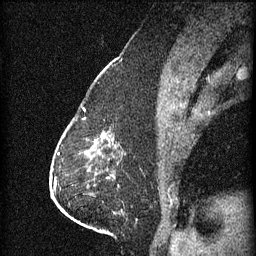
Breast MRI (dynamic contrast-enhanced), one sagittal slice; 3 images stored at this slice position (order not interpretable as contrast timing); 1.5 T; TE 4.2 ms, TR 11 ms; 1.5 mm slice thickness; 256 × 256 image matrix, field of view 180 × 180 mm. Female patient, age 63 years.
Structures marked on this image (semi-automatic segmentation, software-assisted and operator-edited):
- analysis volume of interest (the breast-tissue region the enhancement analysis was run in; not a lesion): bounding box (x1, y1, x2, y2) in pixels: (86, 130, 125, 153)
- tumour enhancement mask (voxels above the 70 % enhancement threshold inside the analysis volume of interest): (92, 134, 105, 151)